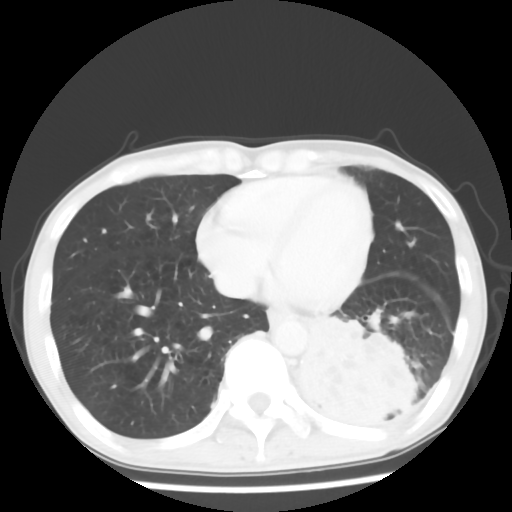
Chest CT, one axial slice; position 20 of 64 along the scan axis; 120 kVp; lung window (W 1500 / L -600 HU); 5 mm slice thickness; 512 × 512 image matrix, field of view 313 × 313 mm. Male patient, age 68 years. Case-level facts recorded for this patient, not image findings: clinical TNM (as recorded): T4 N0 M0.
Outlined on this slice (bounding box drawn by a radiologist):
- lung tumour (recorded histology: squamous cell carcinoma): box from (x=283, y=314) to (x=423, y=439) px